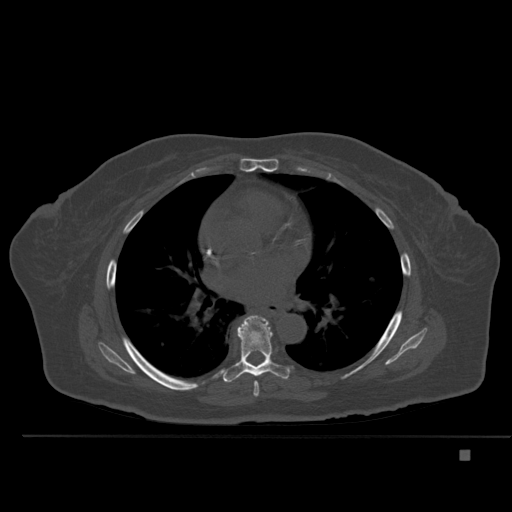
CT including the spine, one axial slice. Position 327 of 477 along the scan axis. Bone window (W 1800 / L 400 HU). 1.5 mm slice thickness. 512 × 512 image matrix, field of view 422 × 422 mm. Female patient, age 74 years. Case-level facts recorded for this patient, not image findings: primary cancer: colon.
Annotated regions visible in this slice (semi-automatically segmented with operator editing):
- T6 vertebra: bounding box [x1, y1, x2, y2] px = [253, 381, 259, 398]
- T7 vertebra: [221, 315, 290, 383]